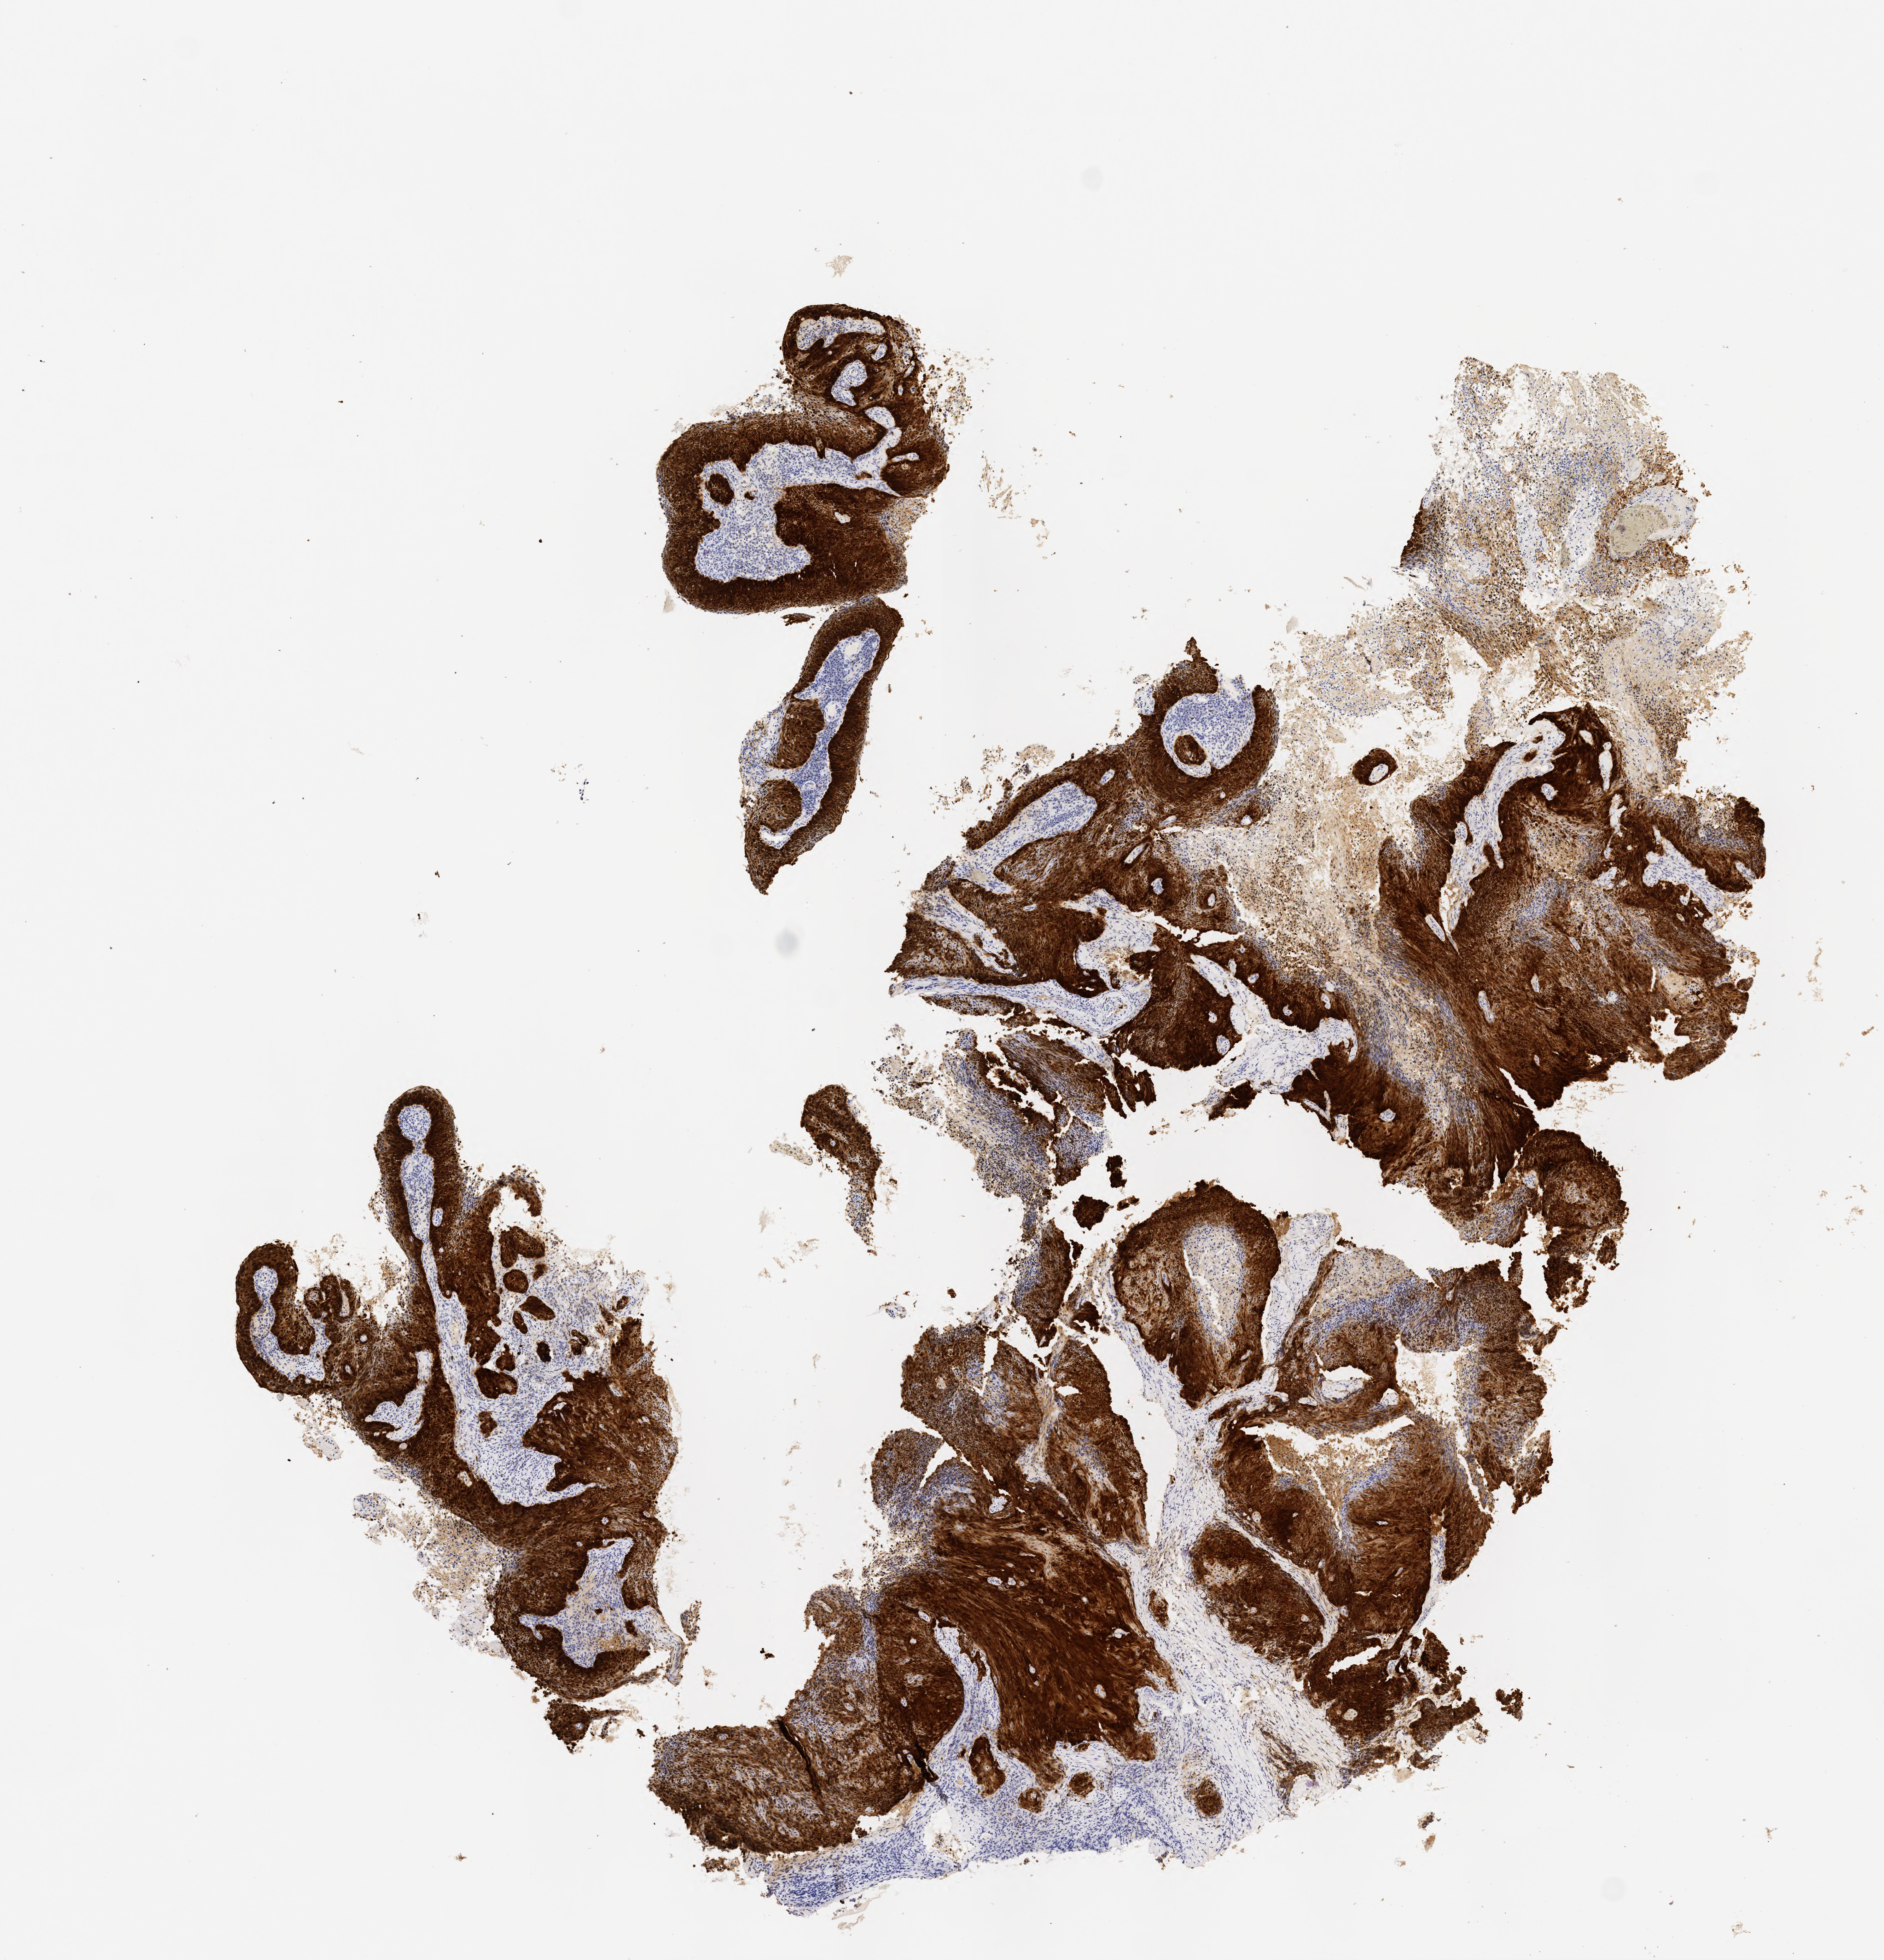
Immunohistochemistry (IHC) whole-slide image stained for p16 (p16INK4a), shown as a low-resolution overview of the whole scanned area (about 6.0 x 6.3 mm). Specimen: tumor tissue. Anatomic site: cervix. Patient female; aged 57.
- diagnosis: Squamous cell carcinoma, large cell, nonkeratinizing, NOS